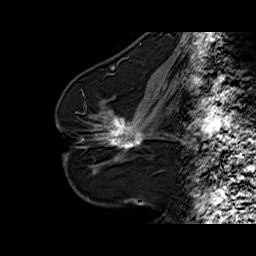
Breast MRI (dynamic contrast-enhanced), one sagittal slice. Slice 31 of 60 in the series (ordered by position). Dynamic contrast-enhanced series, time point 2 of 6 at this slice position (early post-contrast). 1.5 T. TE 6.3 ms, TR 32.5 ms. 4 mm slice thickness. 256 × 256 image matrix. Female patient. Case-level facts recorded for this patient, not image findings: setting: breast cancer imaged before/during neoadjuvant chemotherapy; receptor status: HR-positive, HER2-negative.
Structures marked on this image (semi-automatically segmented with operator editing):
- analysis volume of interest (the breast-tissue region the enhancement analysis was run in; not a lesion): box from (x=94, y=103) to (x=161, y=164) px
- tumour enhancement mask (voxels above the 100 % enhancement threshold inside the analysis volume of interest): (x=108, y=111)–(x=142, y=150)